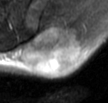
MRI of an extremity soft-tissue mass, one axial slice; slice 25 of 42 in the series (ordered by position); T2-weighted fat-saturated; MR volume resampled by the dataset authors to the PET/CT grid (not the native acquisition matrix); 3.27 mm slice thickness; 108 × 103 image matrix, field of view 105 × 101 mm. Male patient. Case-level facts recorded for this patient, not image findings: histological type: leiomyosarcoma; grade: intermediate; site of the primary tumour: left pelvis.
Annotated regions visible in this slice (expert contour drawn on MRI and transferred to this co-registered scan by the dataset authors):
- gross tumour volume (mass): bounding box (x1, y1, x2, y2) in pixels: (21, 23, 86, 75)